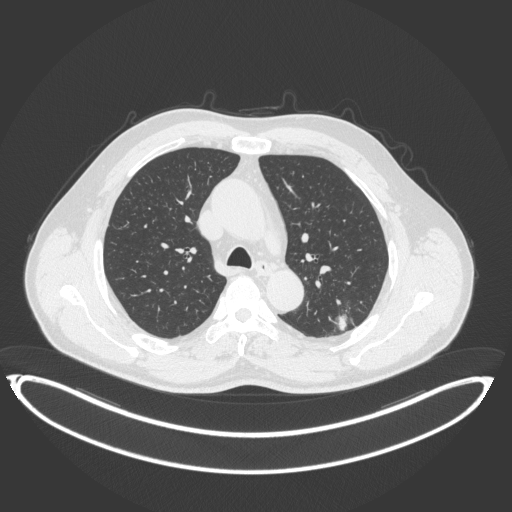
Chest CT, one axial slice; slice 245 of 399 in the series (ordered by position); reconstruction kernel B31f; lung window (W 1500 / L -600 HU); 1 mm slice thickness; 512 × 512 image matrix. Patient: male, 58 years. Case-level facts recorded for this patient, not image findings: clinical TNM (as recorded): T1c N0 M0; histopathological grade: G1-2.
Structures marked on this image (bounding box drawn by a radiologist):
- lung tumour (recorded histology: adenocarcinoma): bounding box [x1, y1, x2, y2] px = [328, 305, 358, 337]